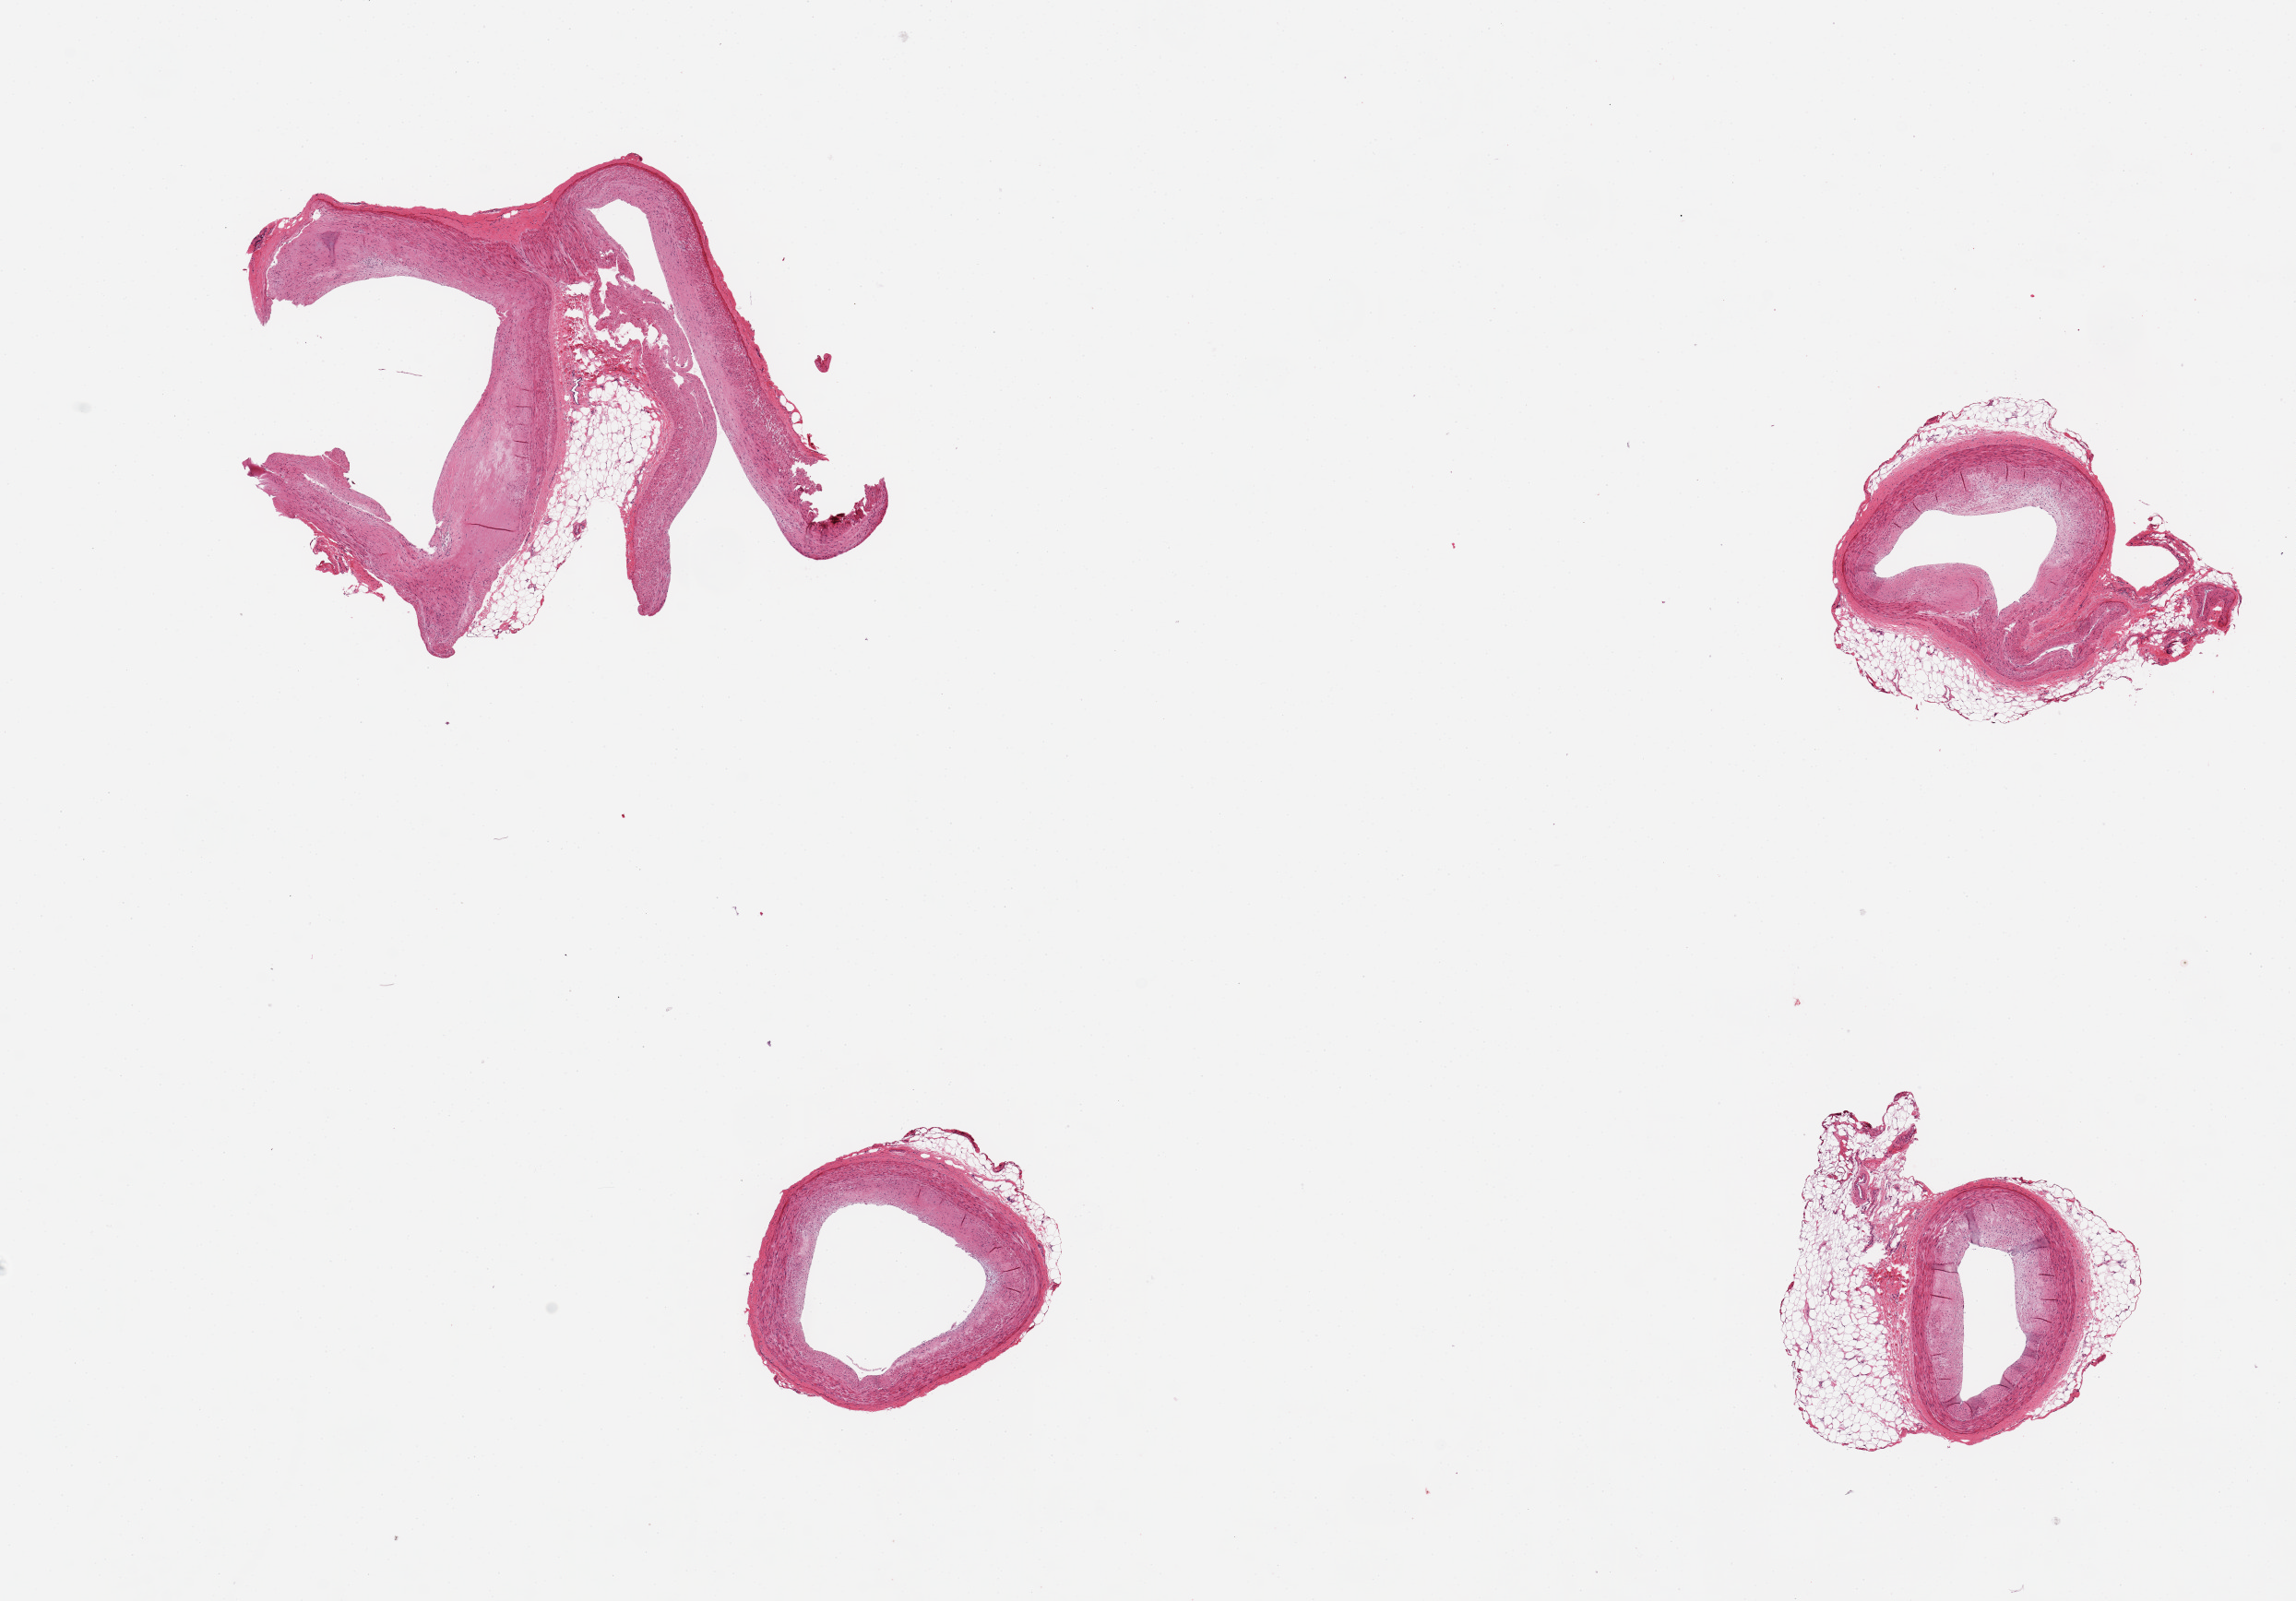
Digitized haematoxylin and eosin-stained section, brightfield, shown as a low-resolution overview of the whole scanned area (about 19.7 x 13.7 mm, from a 20x scan). PAXgene-fixed paraffin-embedded (PFPE) section. Sampled site (target tissue): coronary artery. Tissue donor sample. Donor sex: male.
Review note (as recorded): 4 pieces ~2.5mm d. Several with ~0.5mm discontinuous adherent fat; several with ~20% atherosclerotic narrowing.